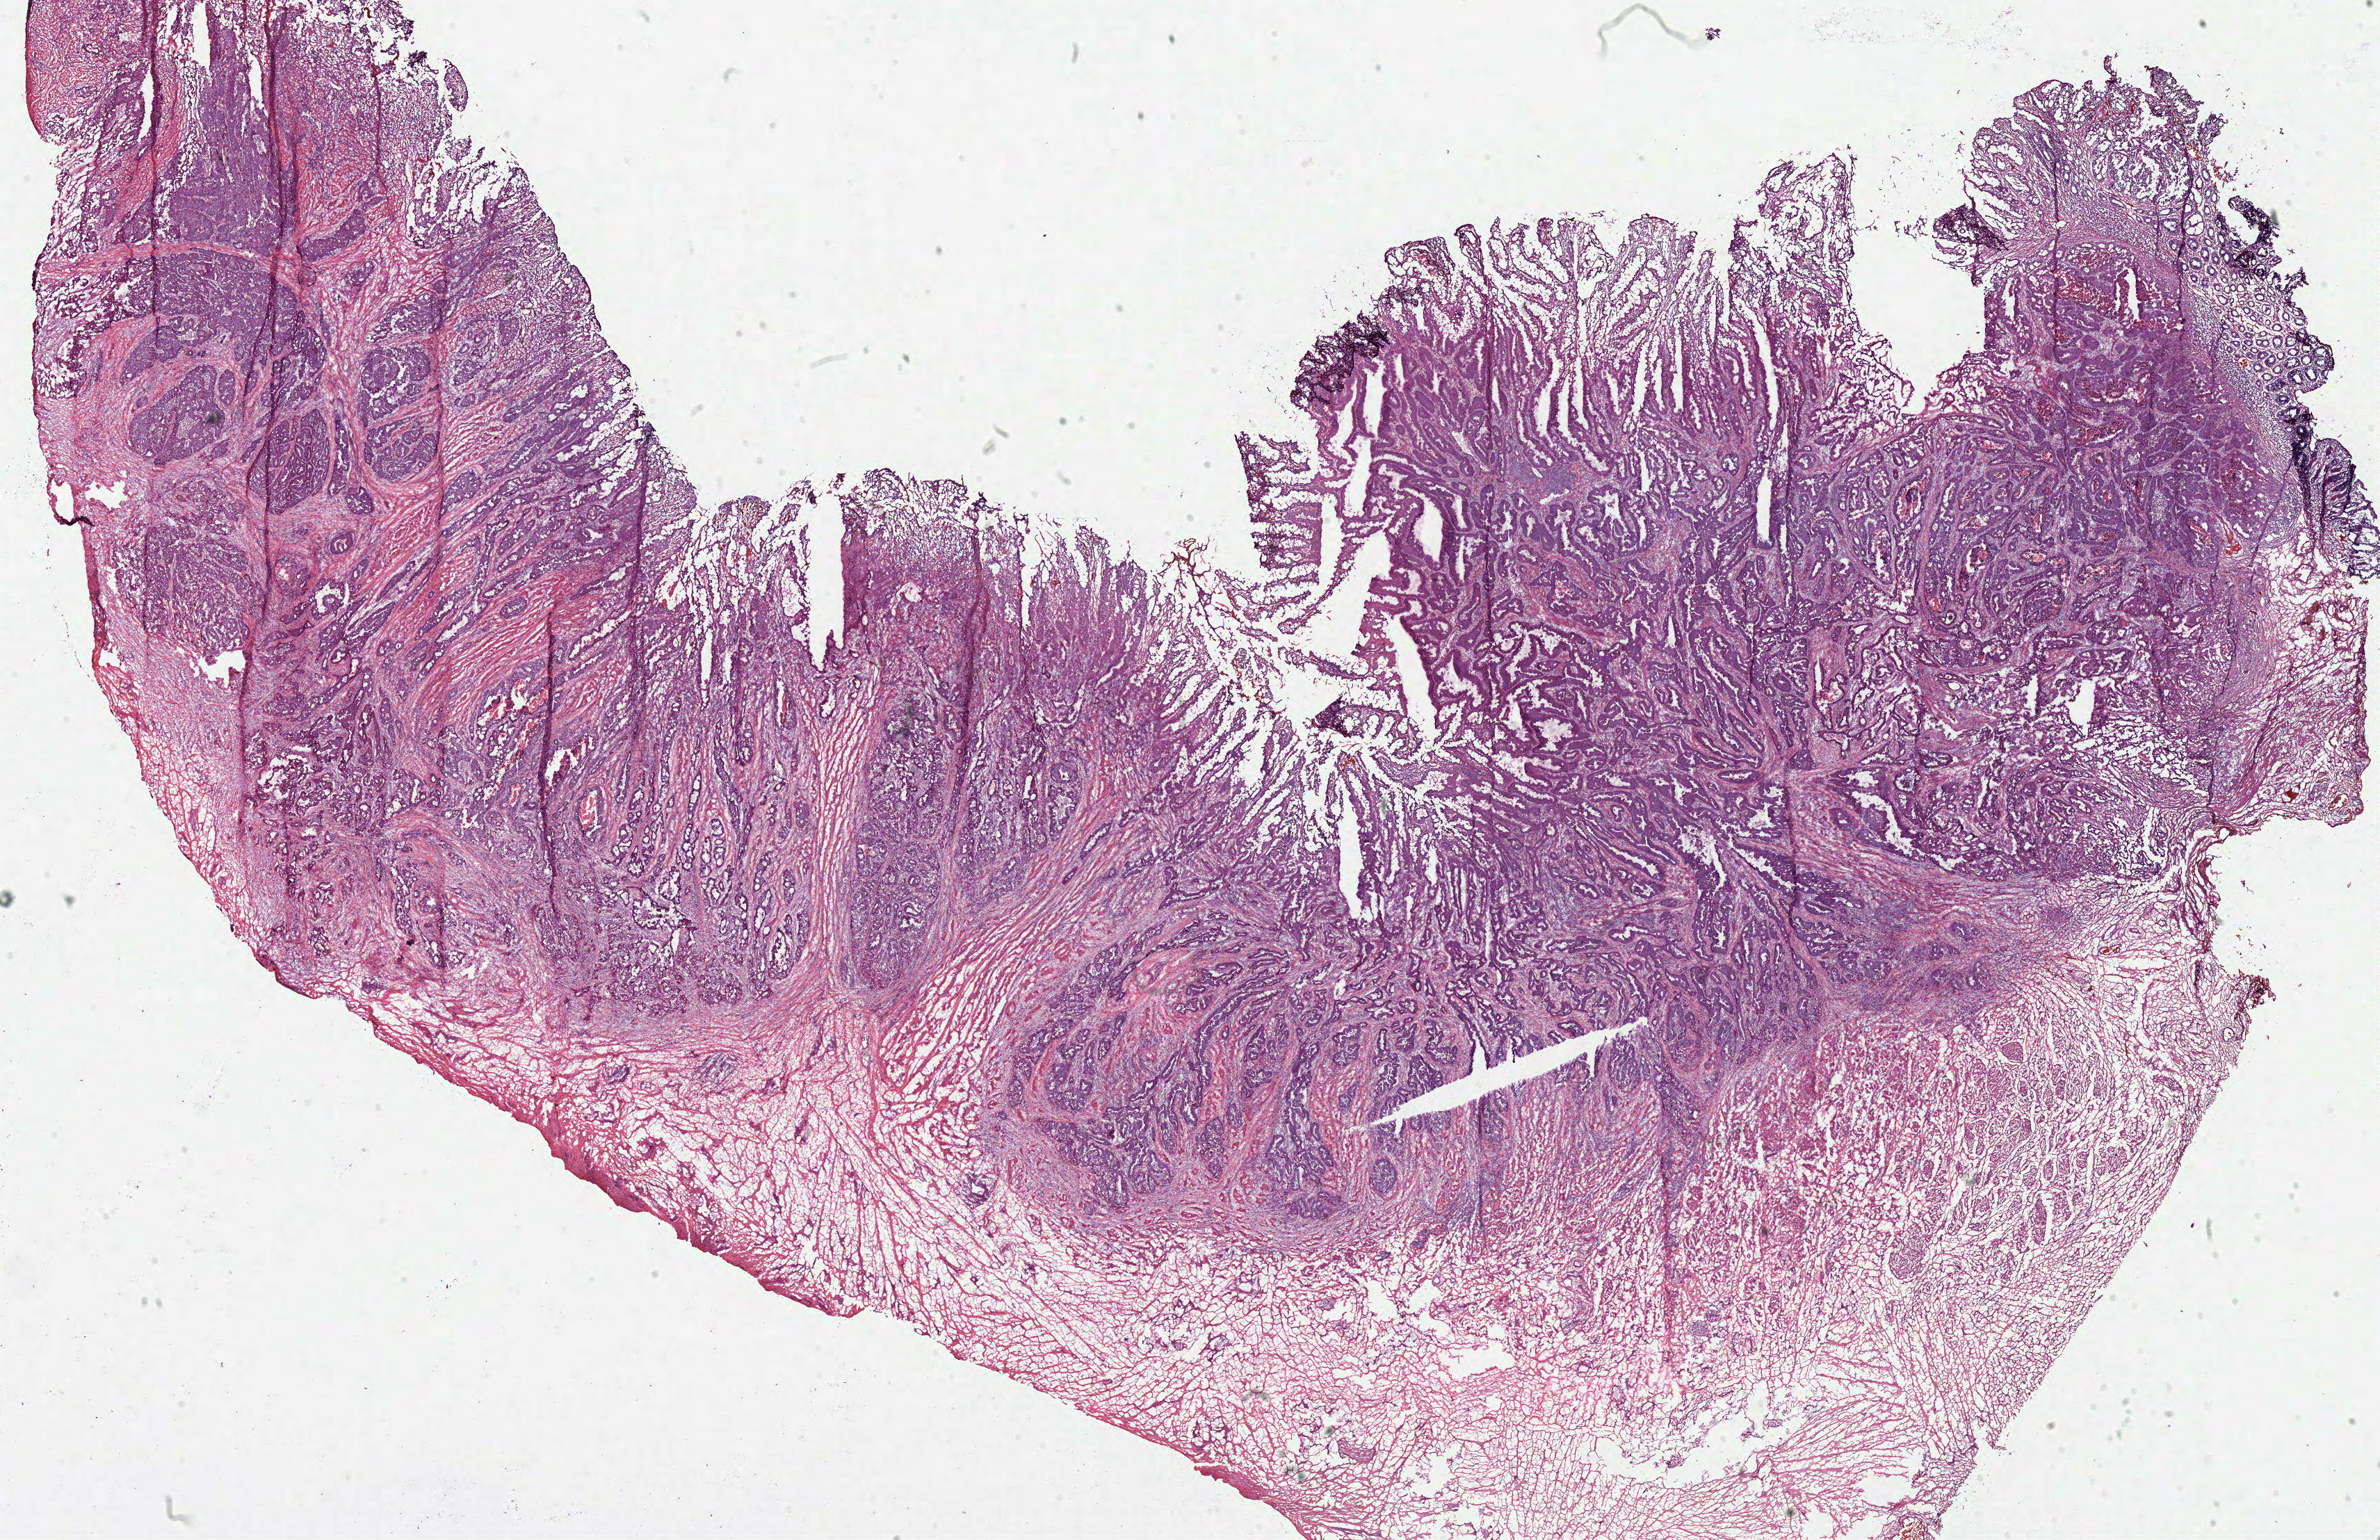
Digitized H&E tissue section (whole slide), a low-resolution overview of the entire scanned area, about 26.9 x 17.4 mm; frozen section from the top of the tissue portion; sample: primary tumour, rectum. Patient: female, age at initial diagnosis 62 years. Composition of this section per pathologist review: tumour cells 65%, tumour nuclei 80%, normal cells 5%, stromal cells 20%, necrosis 10%.
Lymph nodes positive (case pathology): 0 of 2 examined. AJCC pathologic stage: IIA (7th edition). Pathologic diagnosis: Adenocarcinoma, NOS.